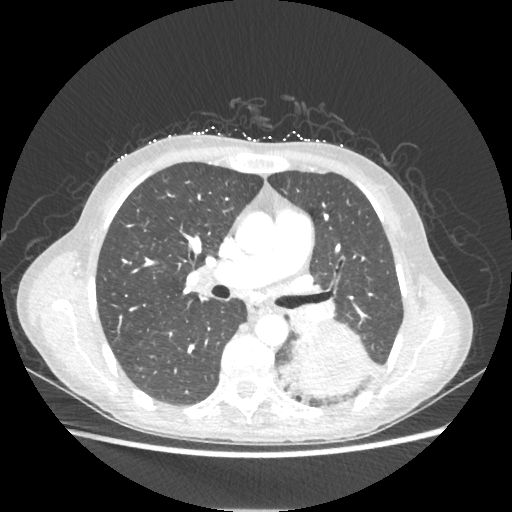
Chest CT, one axial slice; lung window (W 1500 / L -600 HU); 1.25 mm slice thickness; 512 × 512 image matrix, field of view 360 × 360 mm. Female patient, age 53 years. Case-level facts recorded for this patient, not image findings: clinical TNM (as recorded): T3 N0 M0.
Outlined on this slice (rectangle marked by the reading radiologist):
- lung tumour (recorded histology: adenocarcinoma): bounding box <282,324,372,397> (left, top, right, bottom; pixels)